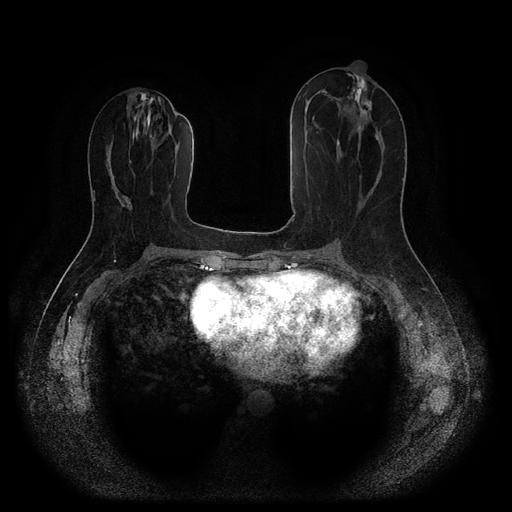
Breast MRI (dynamic contrast-enhanced, multi-phase), one axial slice. Slice 45 of 116 in the series (ordered by position). Dynamic contrast-enhanced series, time point 2 of 5 at this slice position (early post-contrast). 1.5 T. TE 2.6 ms, TR 5.3 ms. 2.2 mm slice thickness. 512 × 512 image matrix, field of view 360 × 360 mm. Female patient, age 53 years.
Structures marked on this image (semi-automatic segmentation, software-assisted and operator-edited):
- breast lesion (labelled 'tumour' in the annotation; benign lesions carry a separate 'benign' label): bounding box (x1, y1, x2, y2) in pixels: (360, 101, 372, 114)